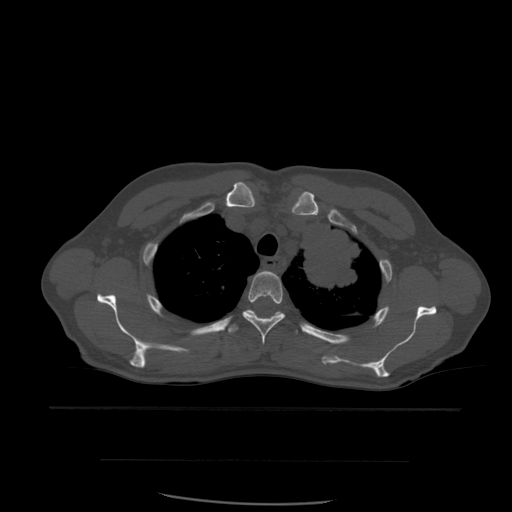
CT including the spine, one axial slice. Slice 440 of 574 in the series (ordered by position). Bone window (W 1800 / L 400 HU). 512 × 512 image matrix, field of view 392 × 392 mm. Patient age 48 years. From the clinical record (not read from this slice): primary cancer: lung.
Annotated regions visible in this slice (semi-automatic segmentation, software-assisted and operator-edited):
- T3 vertebra: bounding box <243,271,285,345> (left, top, right, bottom; pixels)
- T4 vertebra: <228,310,298,334>